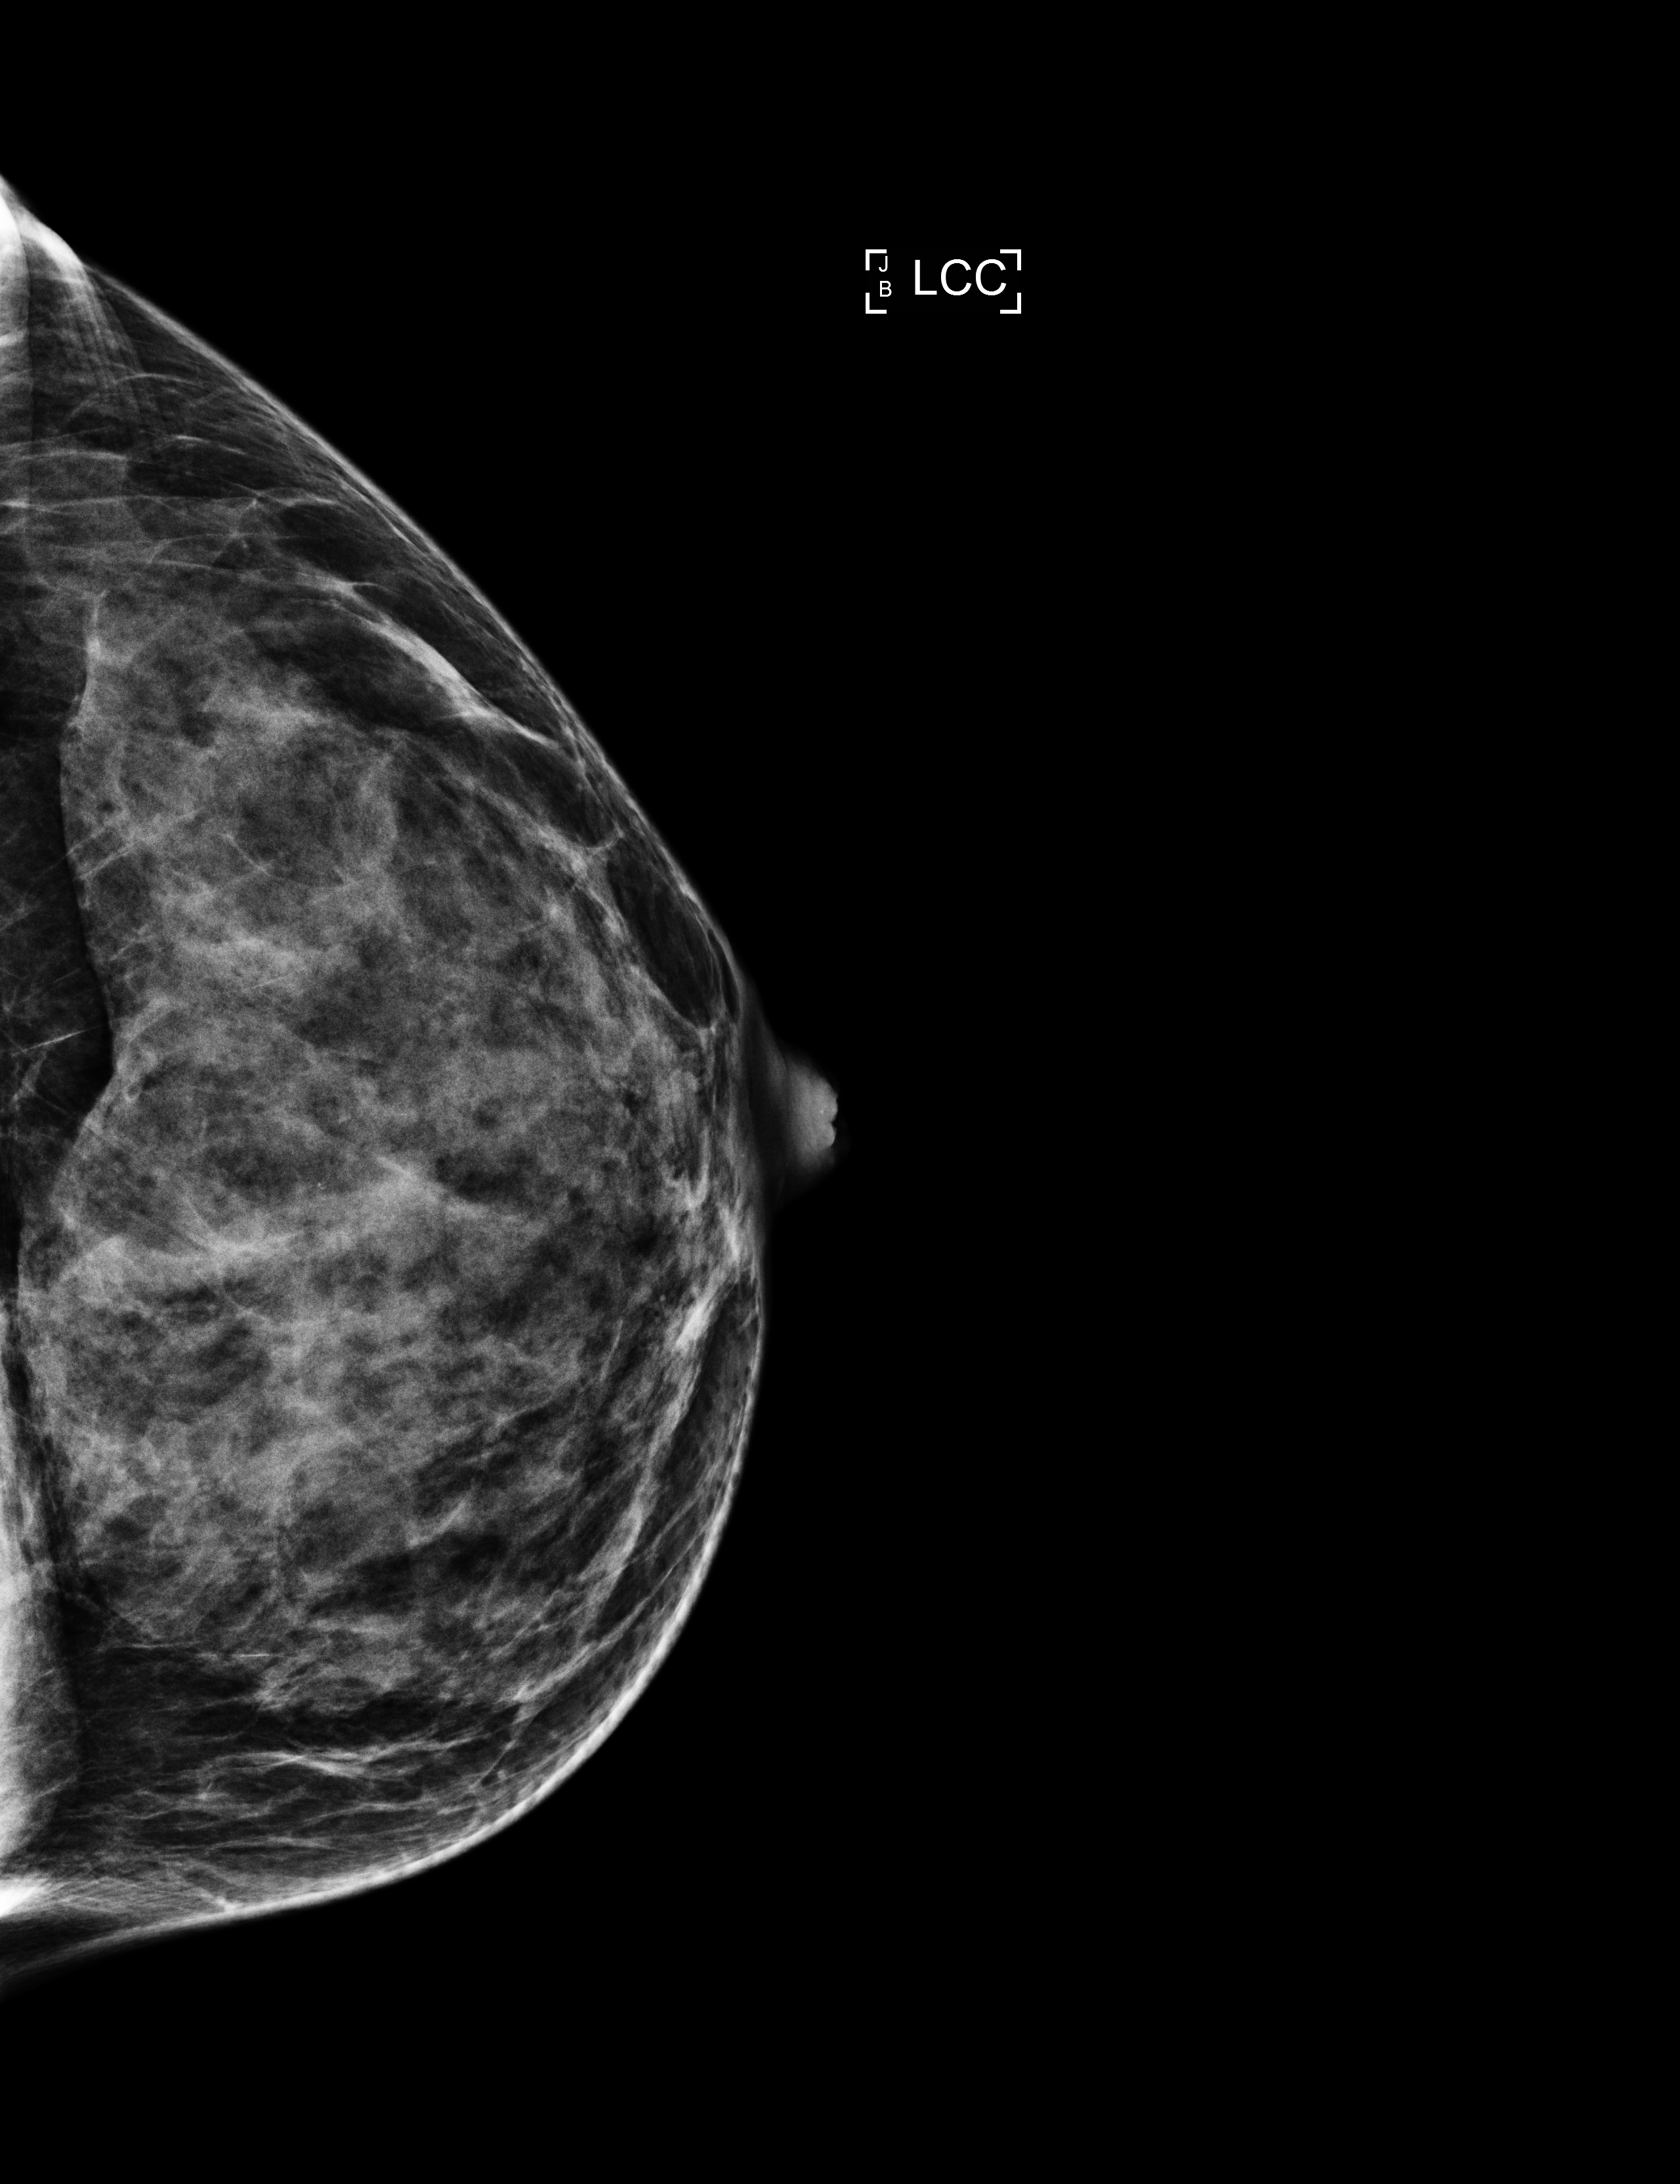
Digital mammogram (FFDM), left breast, CC view, screening examination. Patient aged 46 years (female).
Breast density at the screening exam (both breasts): extremely dense (BI-RADS density category d). Final BI-RADS category for the screening round (tomosynthesis exam, both breasts): category 1. Recall: no recall after this screen.